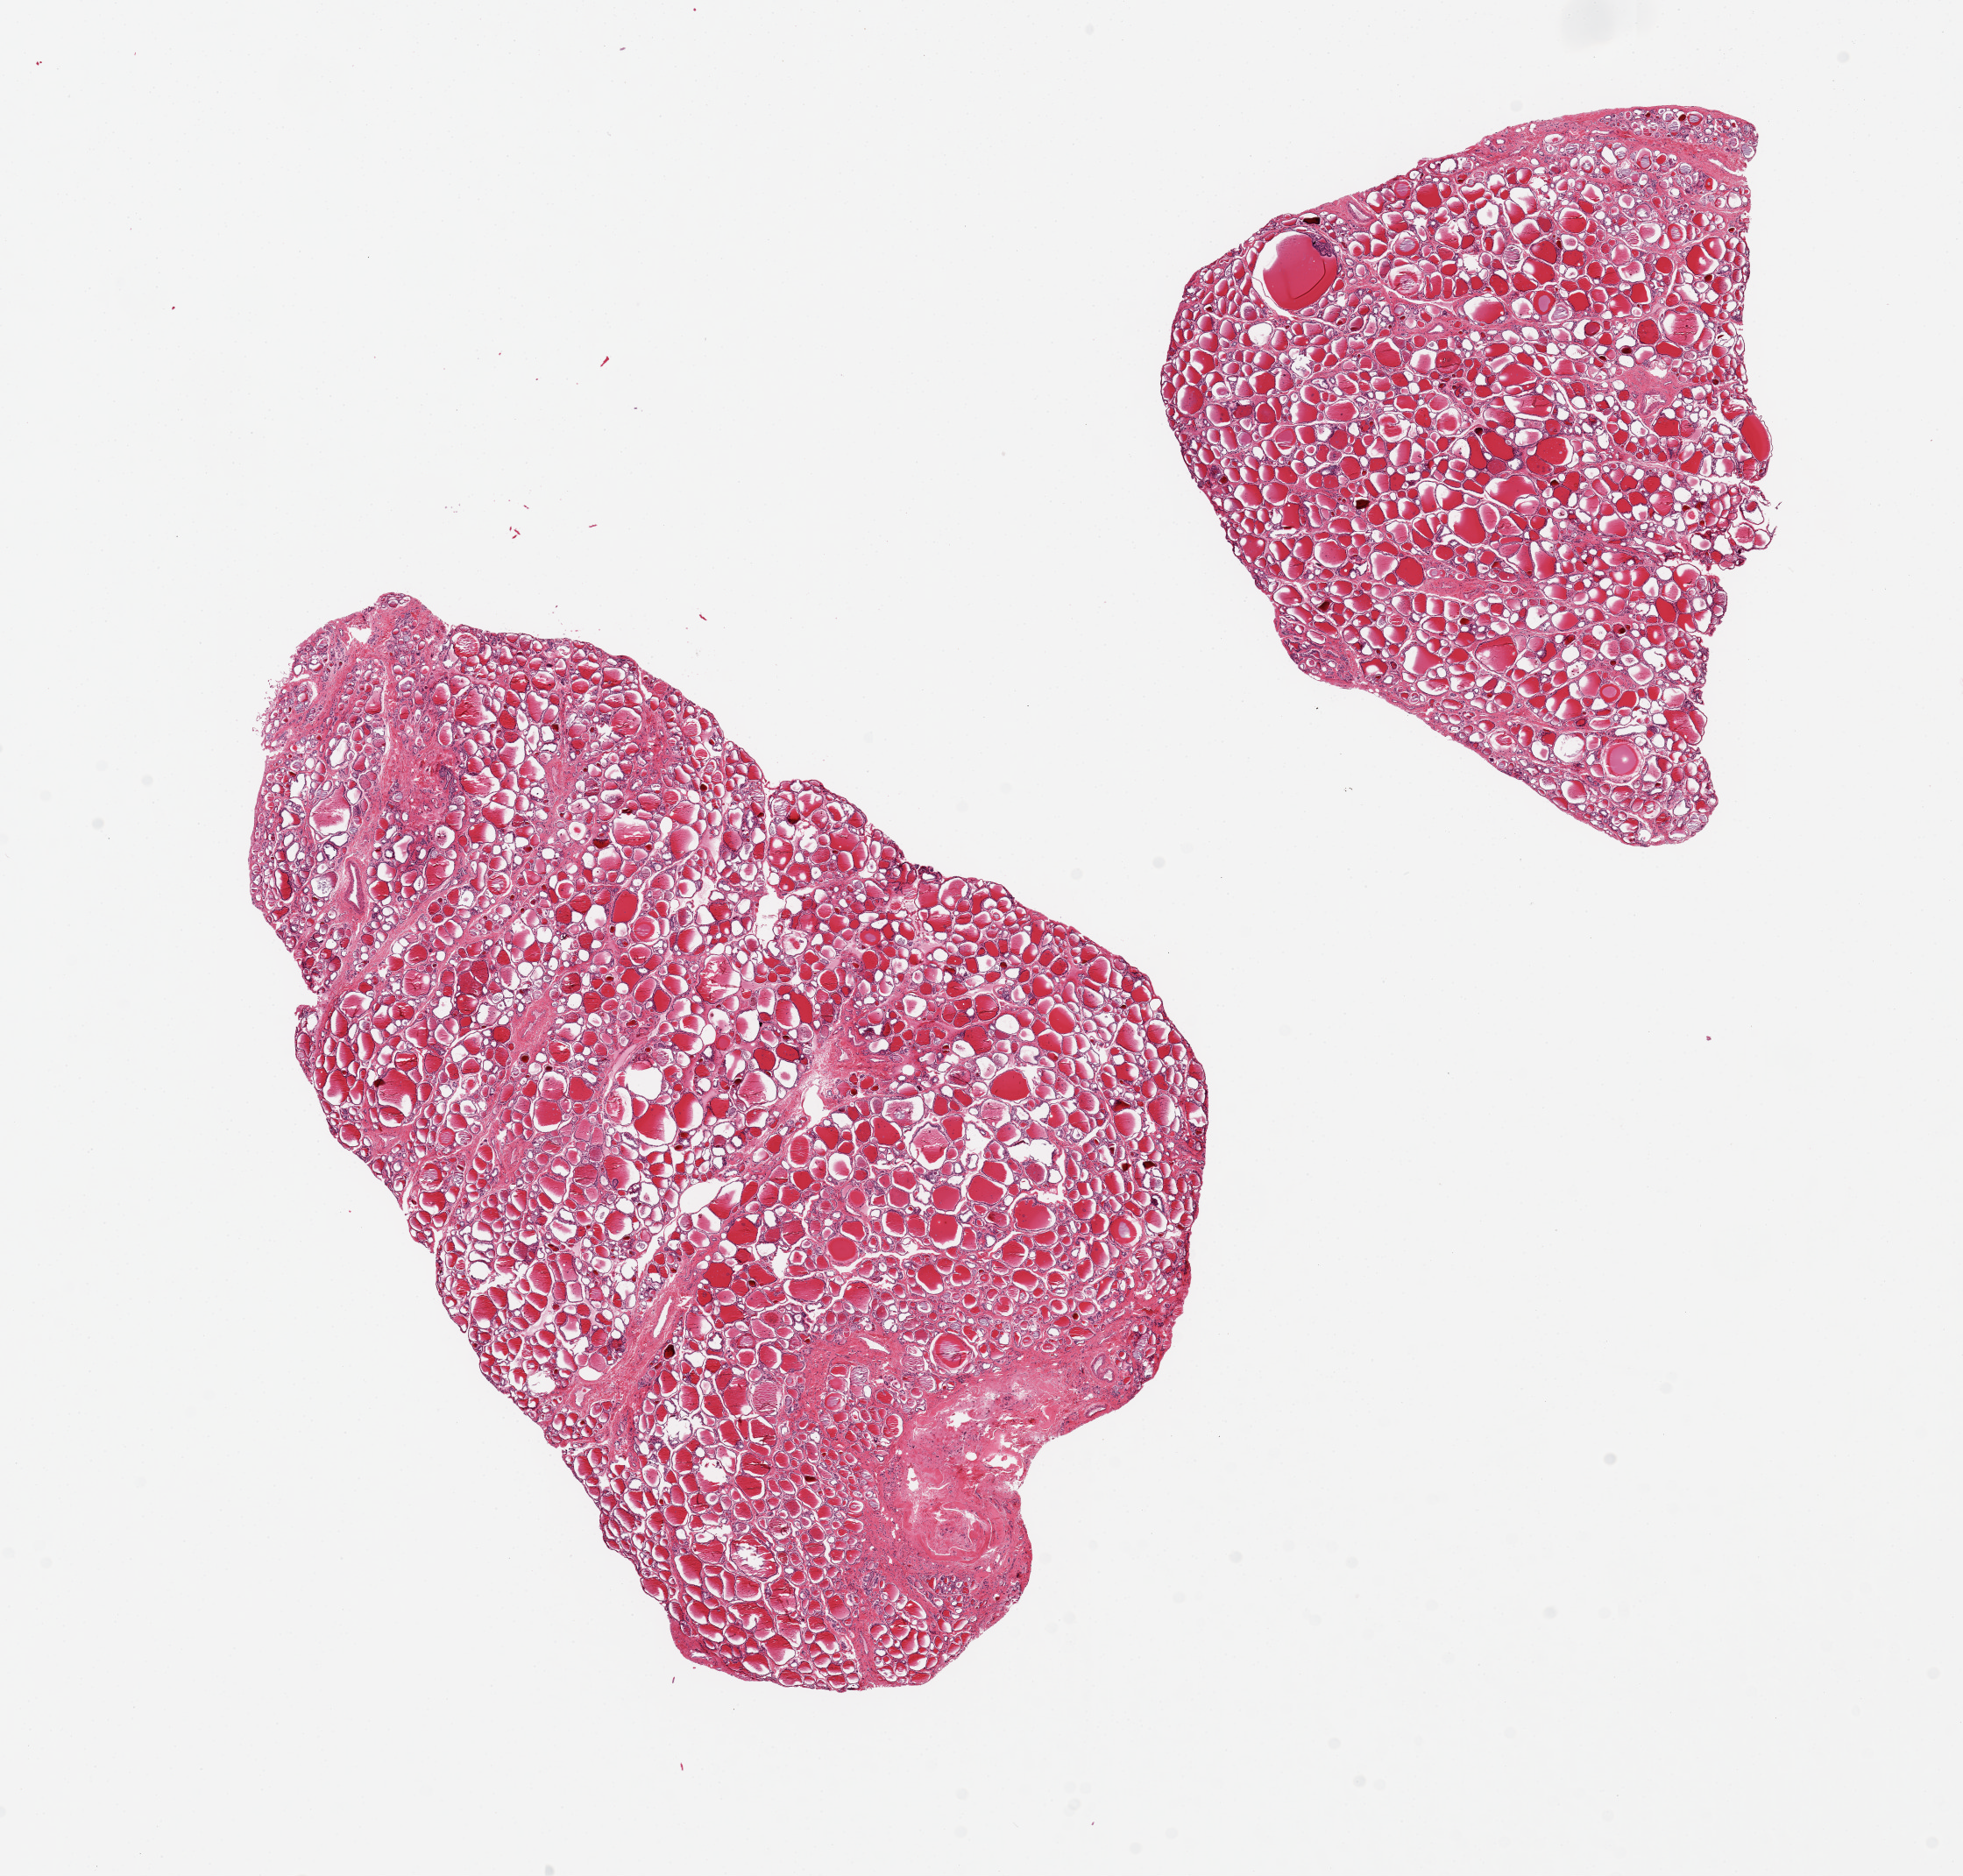
Digitized haematoxylin and eosin-stained section, brightfield, a low-resolution overview of the entire scanned area, about 17.7 x 16.9 mm (from a 20x scan); PAXgene-fixed paraffin-embedded (PFPE) section; section of thyroid (target tissue); tissue donor sample. Female donor.
Pathologist's review note for this sample: 2 pieces, 11x7 & 7x5.5mm; 1mm colloid cyst in one aliquot; 2x1mm focus of fibrous tissue in other aliquot.